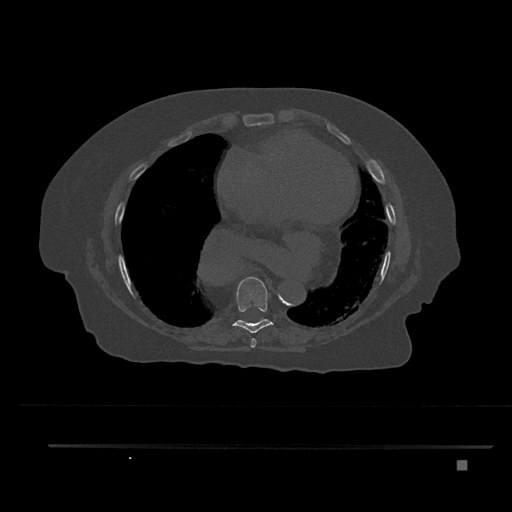
CT including the spine, one axial slice; position 440 of 797 along the scan axis; bone window (W 1800 / L 400 HU); 0.5 mm slice thickness; 512 × 512 image matrix, field of view 437 × 437 mm. Patient: female, 76 years. From the clinical record (not read from this slice): primary cancer: lung.
Annotated regions visible in this slice (semi-automatic segmentation, software-assisted and operator-edited):
- T7 vertebra: bounding box (x1, y1, x2, y2) in pixels: (250, 338, 256, 348)
- T8 vertebra: (233, 277, 274, 333)